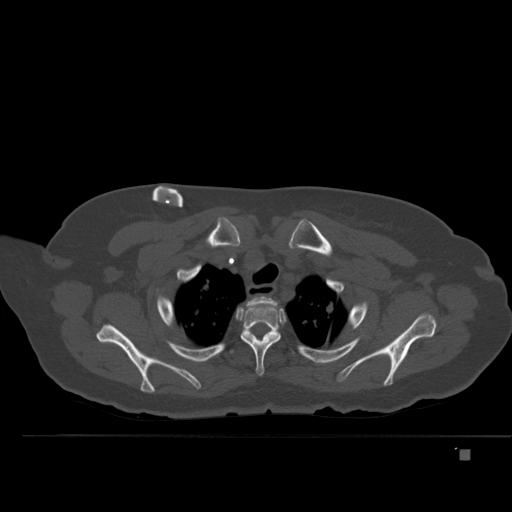
CT including the spine, one axial slice. Position 390 of 477 along the scan axis. Bone window (W 1800 / L 400 HU). 1.5 mm slice thickness. 512 × 512 image matrix, field of view 422 × 422 mm. Female patient, age 74 years. From the clinical record (not read from this slice): primary cancer: colon.
Structures marked on this image (semi-automatically segmented with operator editing):
- T1 vertebra: bounding box [x1, y1, x2, y2] px = [237, 296, 276, 319]
- T2 vertebra: [237, 305, 285, 376]
- T3 vertebra: [230, 332, 280, 353]